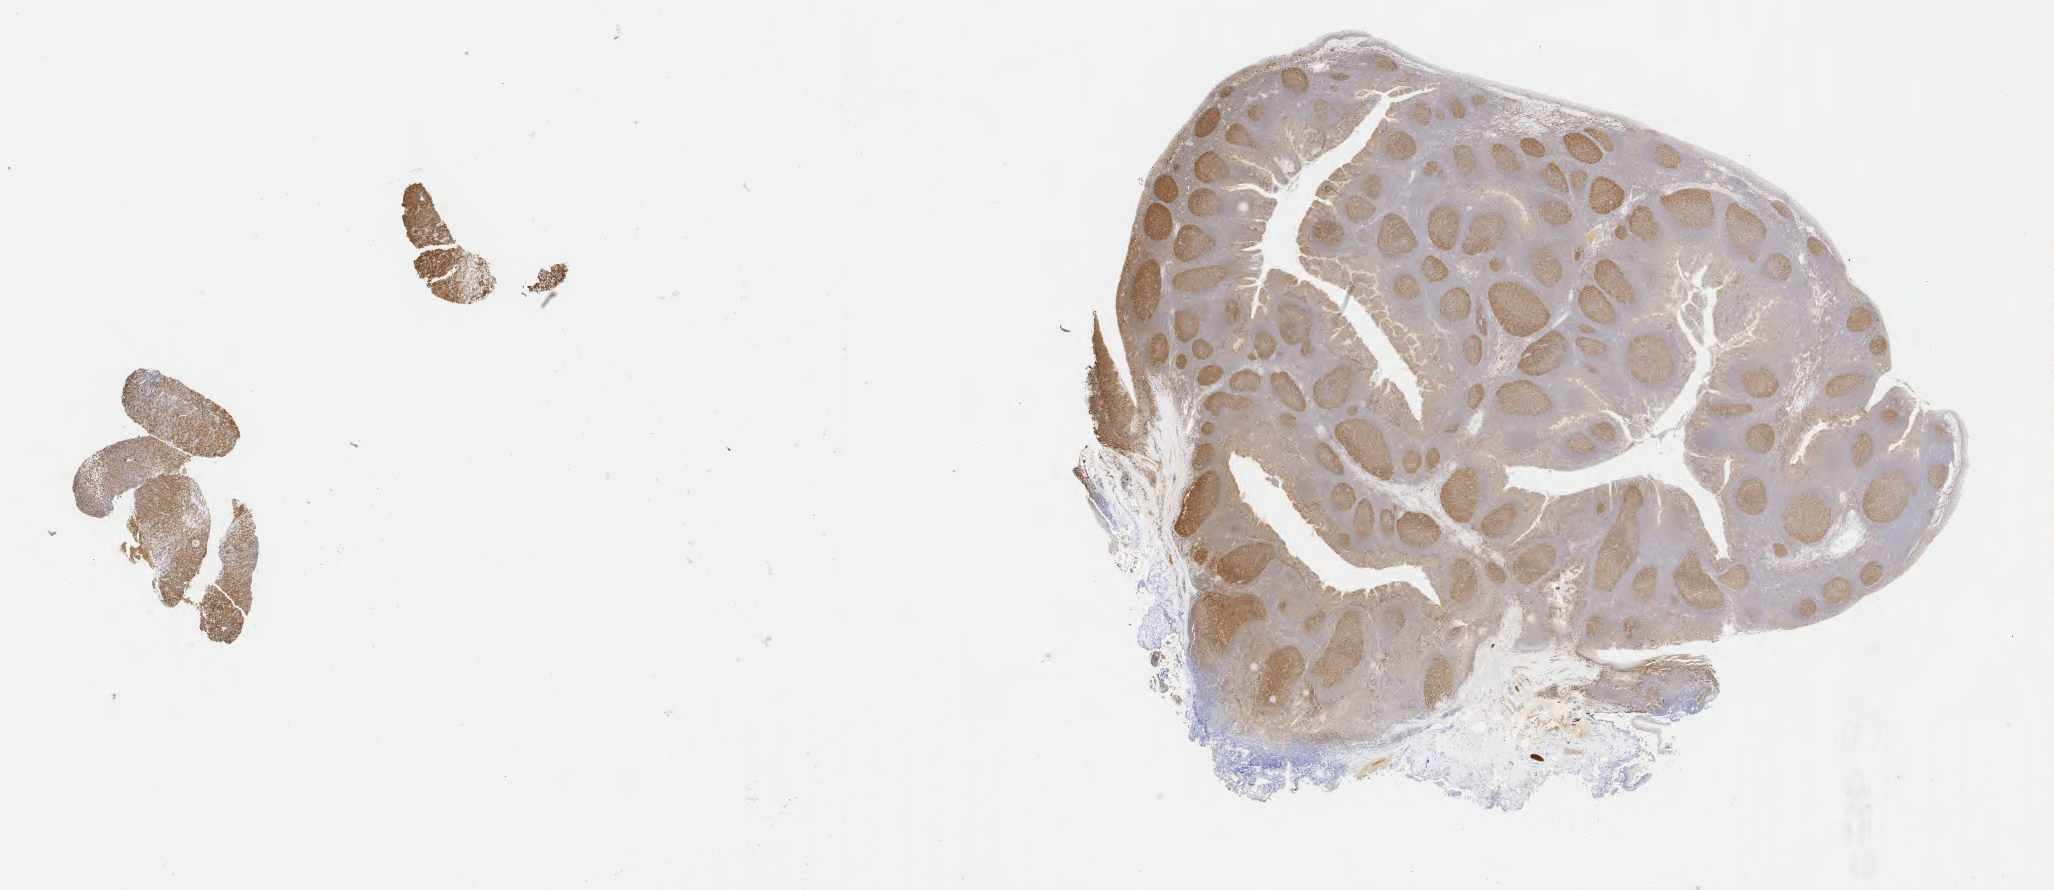
IHC for BCL6, whole-slide image, shown as a low-resolution overview of the whole scanned area (about 33.2 x 14.4 mm). Specimen: tumor tissue. Anatomic site: lymph node. Patient: male, aged 54.
Diagnosis: Diffuse large B-cell lymphoma, NOS.